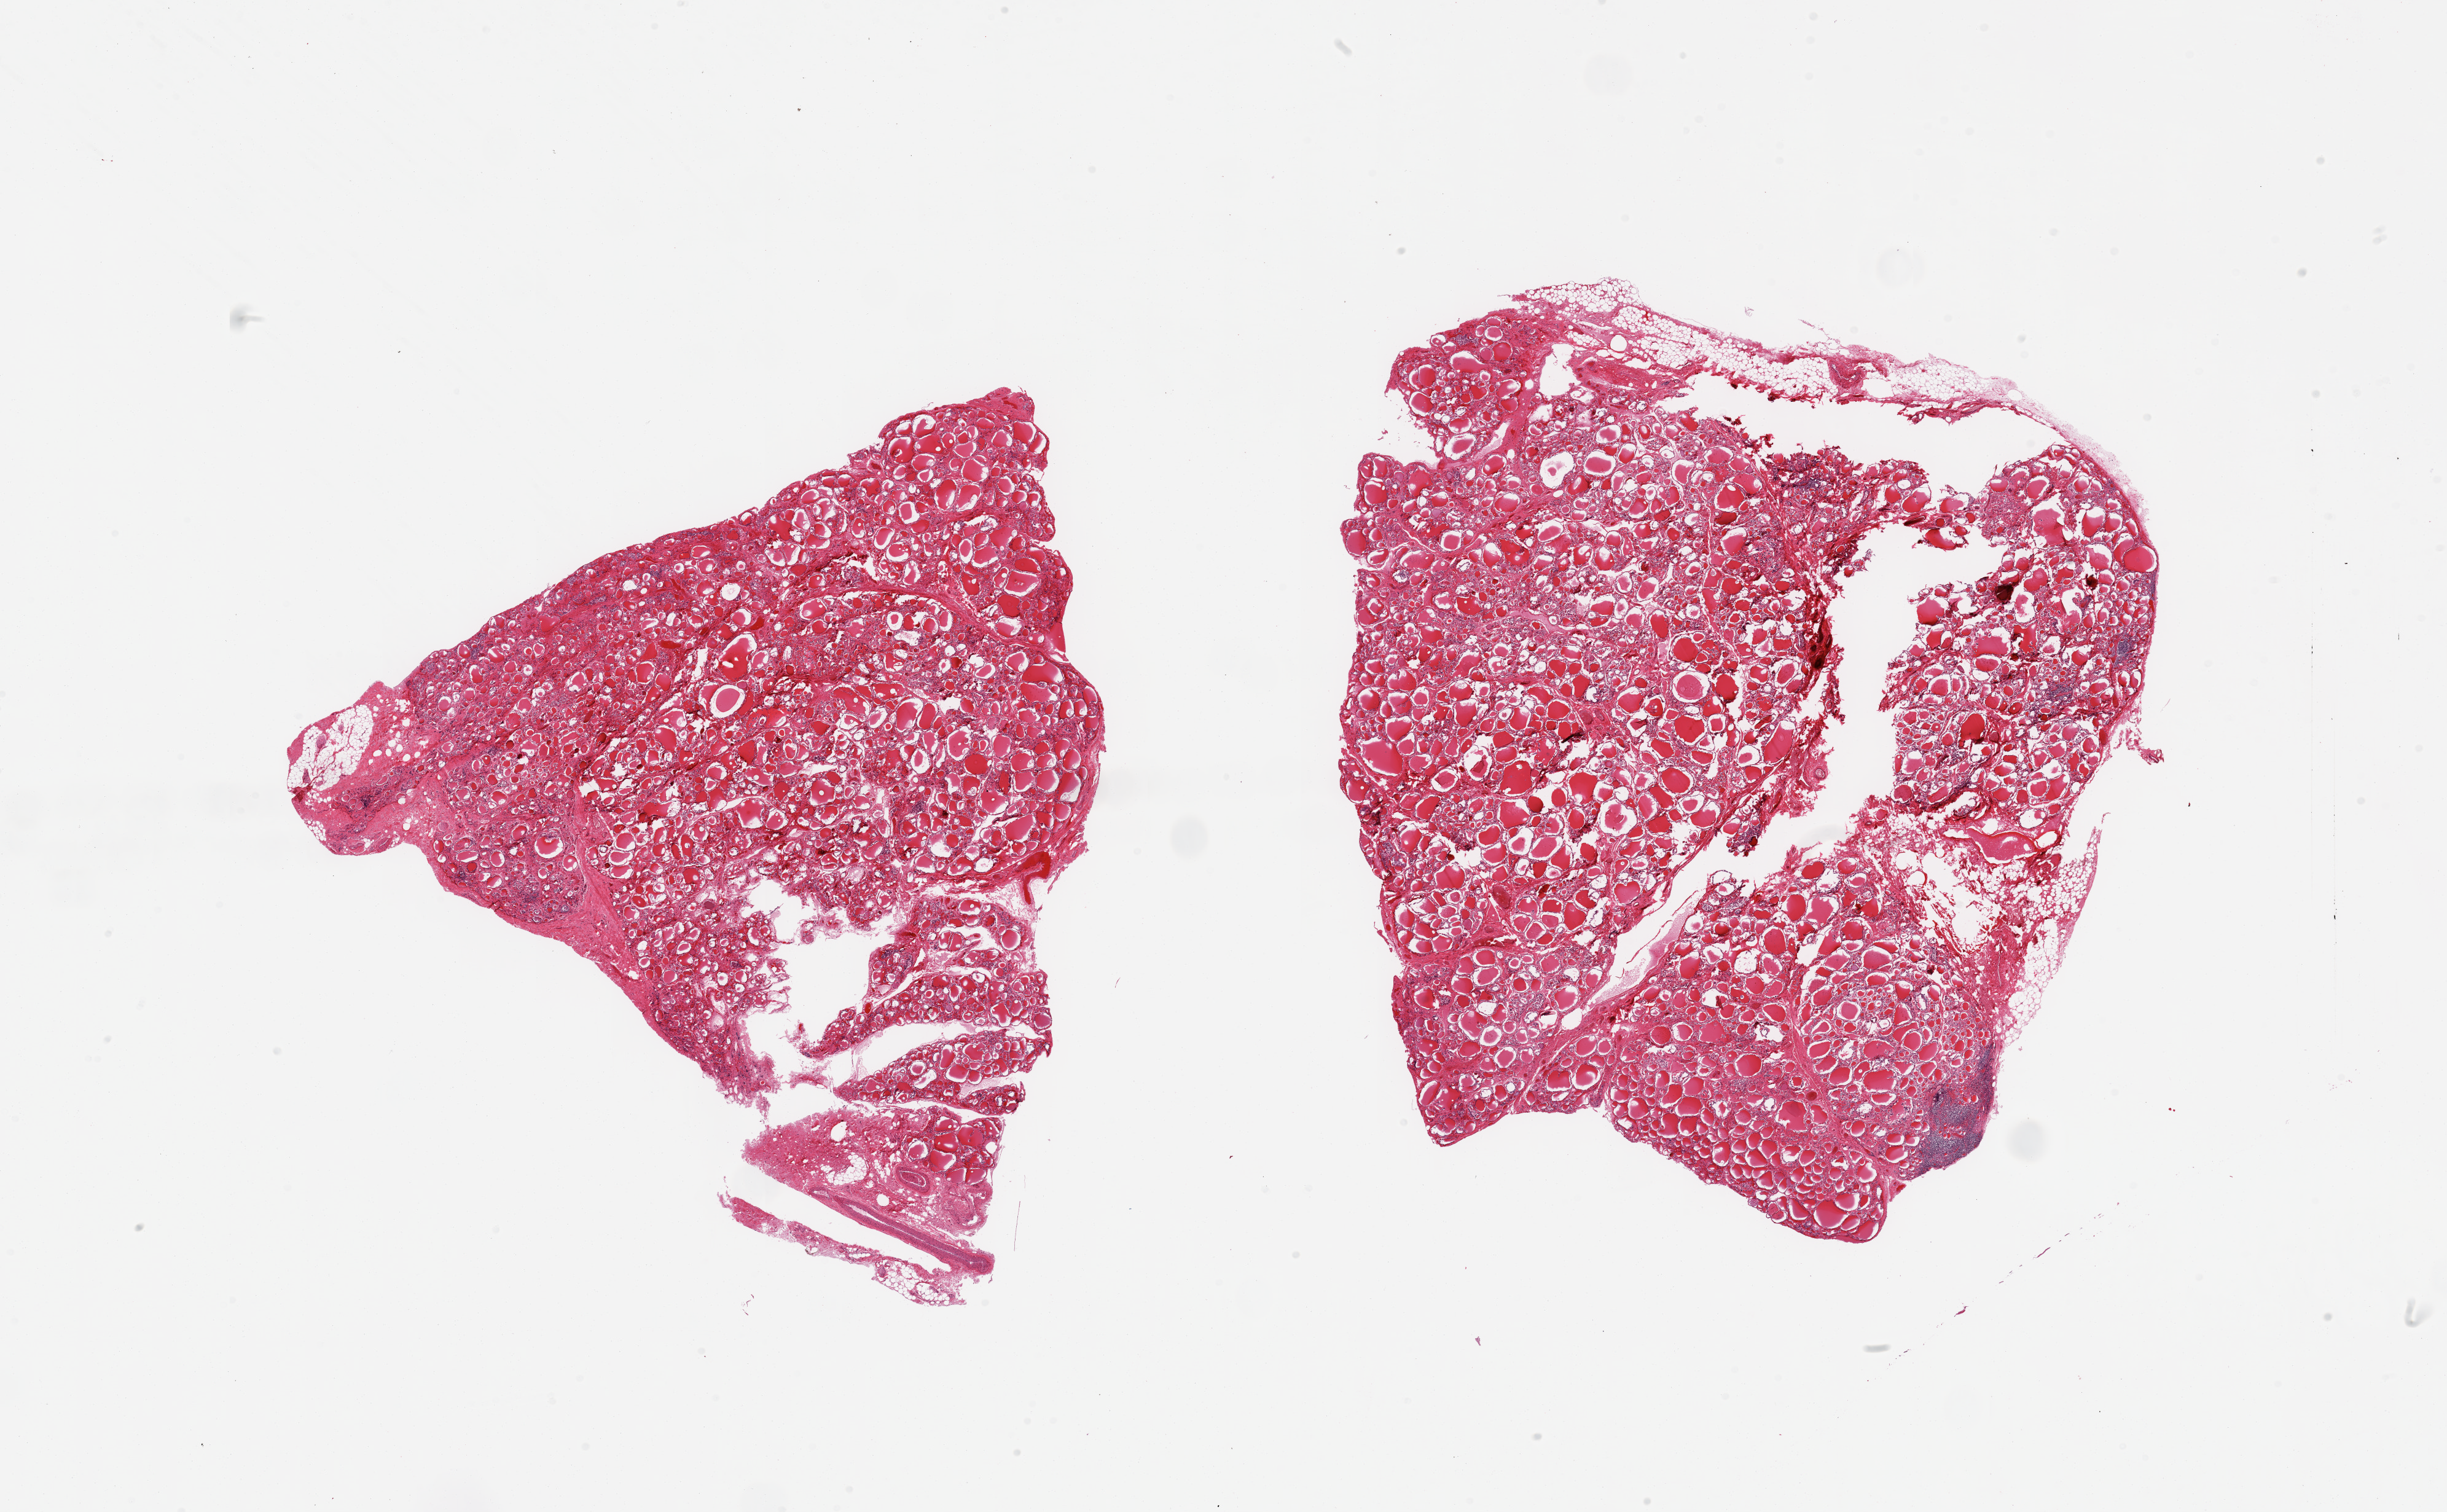
H&E whole-slide image, a low-resolution overview of the entire scanned area, about 31.5 x 19.5 mm (slide scanned at 20x), PAXgene-fixed, paraffin-embedded tissue, target tissue: thyroid, tissue donor sample.
Pathologist's review note for this sample: 2 pieces; 1 focal lymphoid collection [1.7mm] on edge.